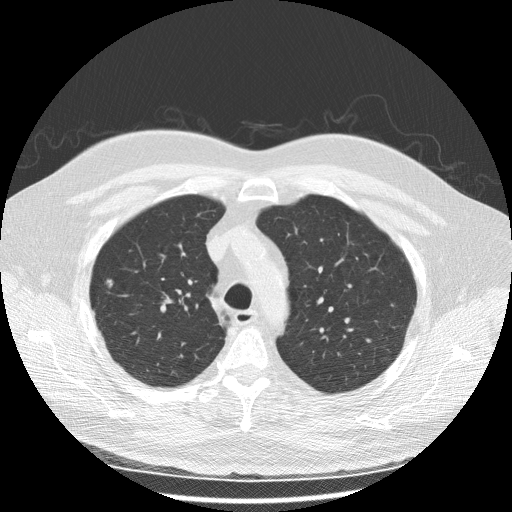
Low-dose screening chest CT, one axial slice; position 187 of 243 along the scan axis; reconstruction kernel STANDARD; 120 kVp; lung window (W 1500 / L -600 HU); 2.5 mm slice thickness; 512 × 512 image matrix, field of view 380 × 380 mm.
Annotated regions visible in this slice (outlined manually by an expert reader):
- lesion 1 (tumor, upper lobe of right lung): box from (x=106, y=279) to (x=113, y=288) px